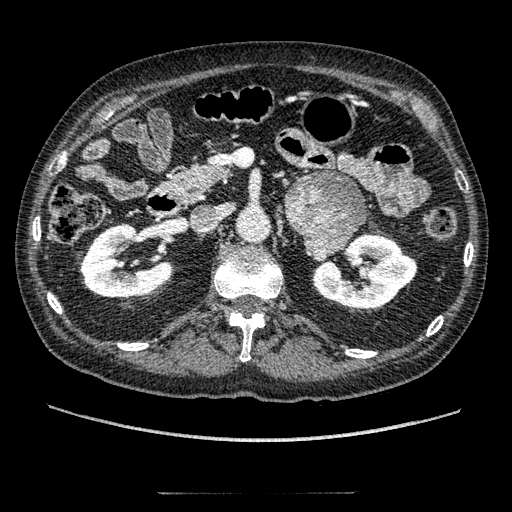
Contrast-enhanced abdominal CT, one axial slice; position 105 of 274 along the scan axis; reconstruction kernel STANDARD; 120 kVp; intravenous contrast given; soft-tissue window (W 400 / L 40 HU); 1.25 mm slice thickness; 512 × 512 image matrix, field of view 381 × 381 mm. Male patient, age 69 years. Case-level facts recorded for this patient, not image findings: diagnosis: adrenocortical carcinoma; tumour side: left adrenal; tumour size at pathology: 6.1 cm; Ki-67 index: 10 %; stage (as recorded): 3.
Annotated regions visible in this slice (semi-automatic segmentation, software-assisted and operator-edited):
- mass: bounding box <287,171,365,258> (left, top, right, bottom; pixels)